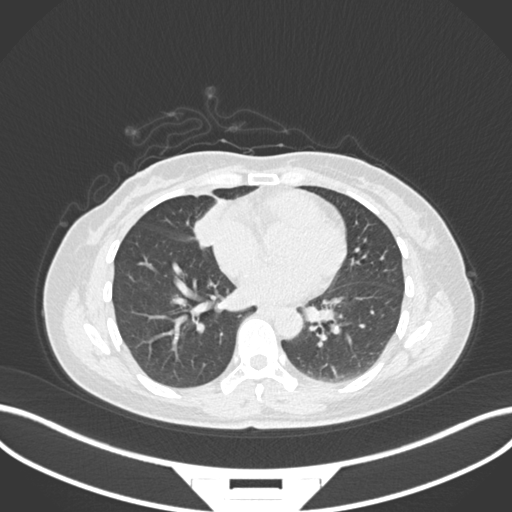
Chest CT, one axial slice. Slice 64 of 171 in the series (ordered by position). Reconstruction kernel B30f. Lung window (W 1500 / L -600 HU). 1 mm slice thickness. 512 × 512 image matrix, field of view 400 × 400 mm. Female patient, age 43 years. Case-level facts recorded for this patient, not image findings: clinical TNM (as recorded): T1c N3 M1; histopathological grade: G1.
Structures marked on this image (bounding box drawn by a radiologist):
- lung tumour (recorded histology: adenocarcinoma): bounding box (x1, y1, x2, y2) in pixels: (187, 201, 223, 251)